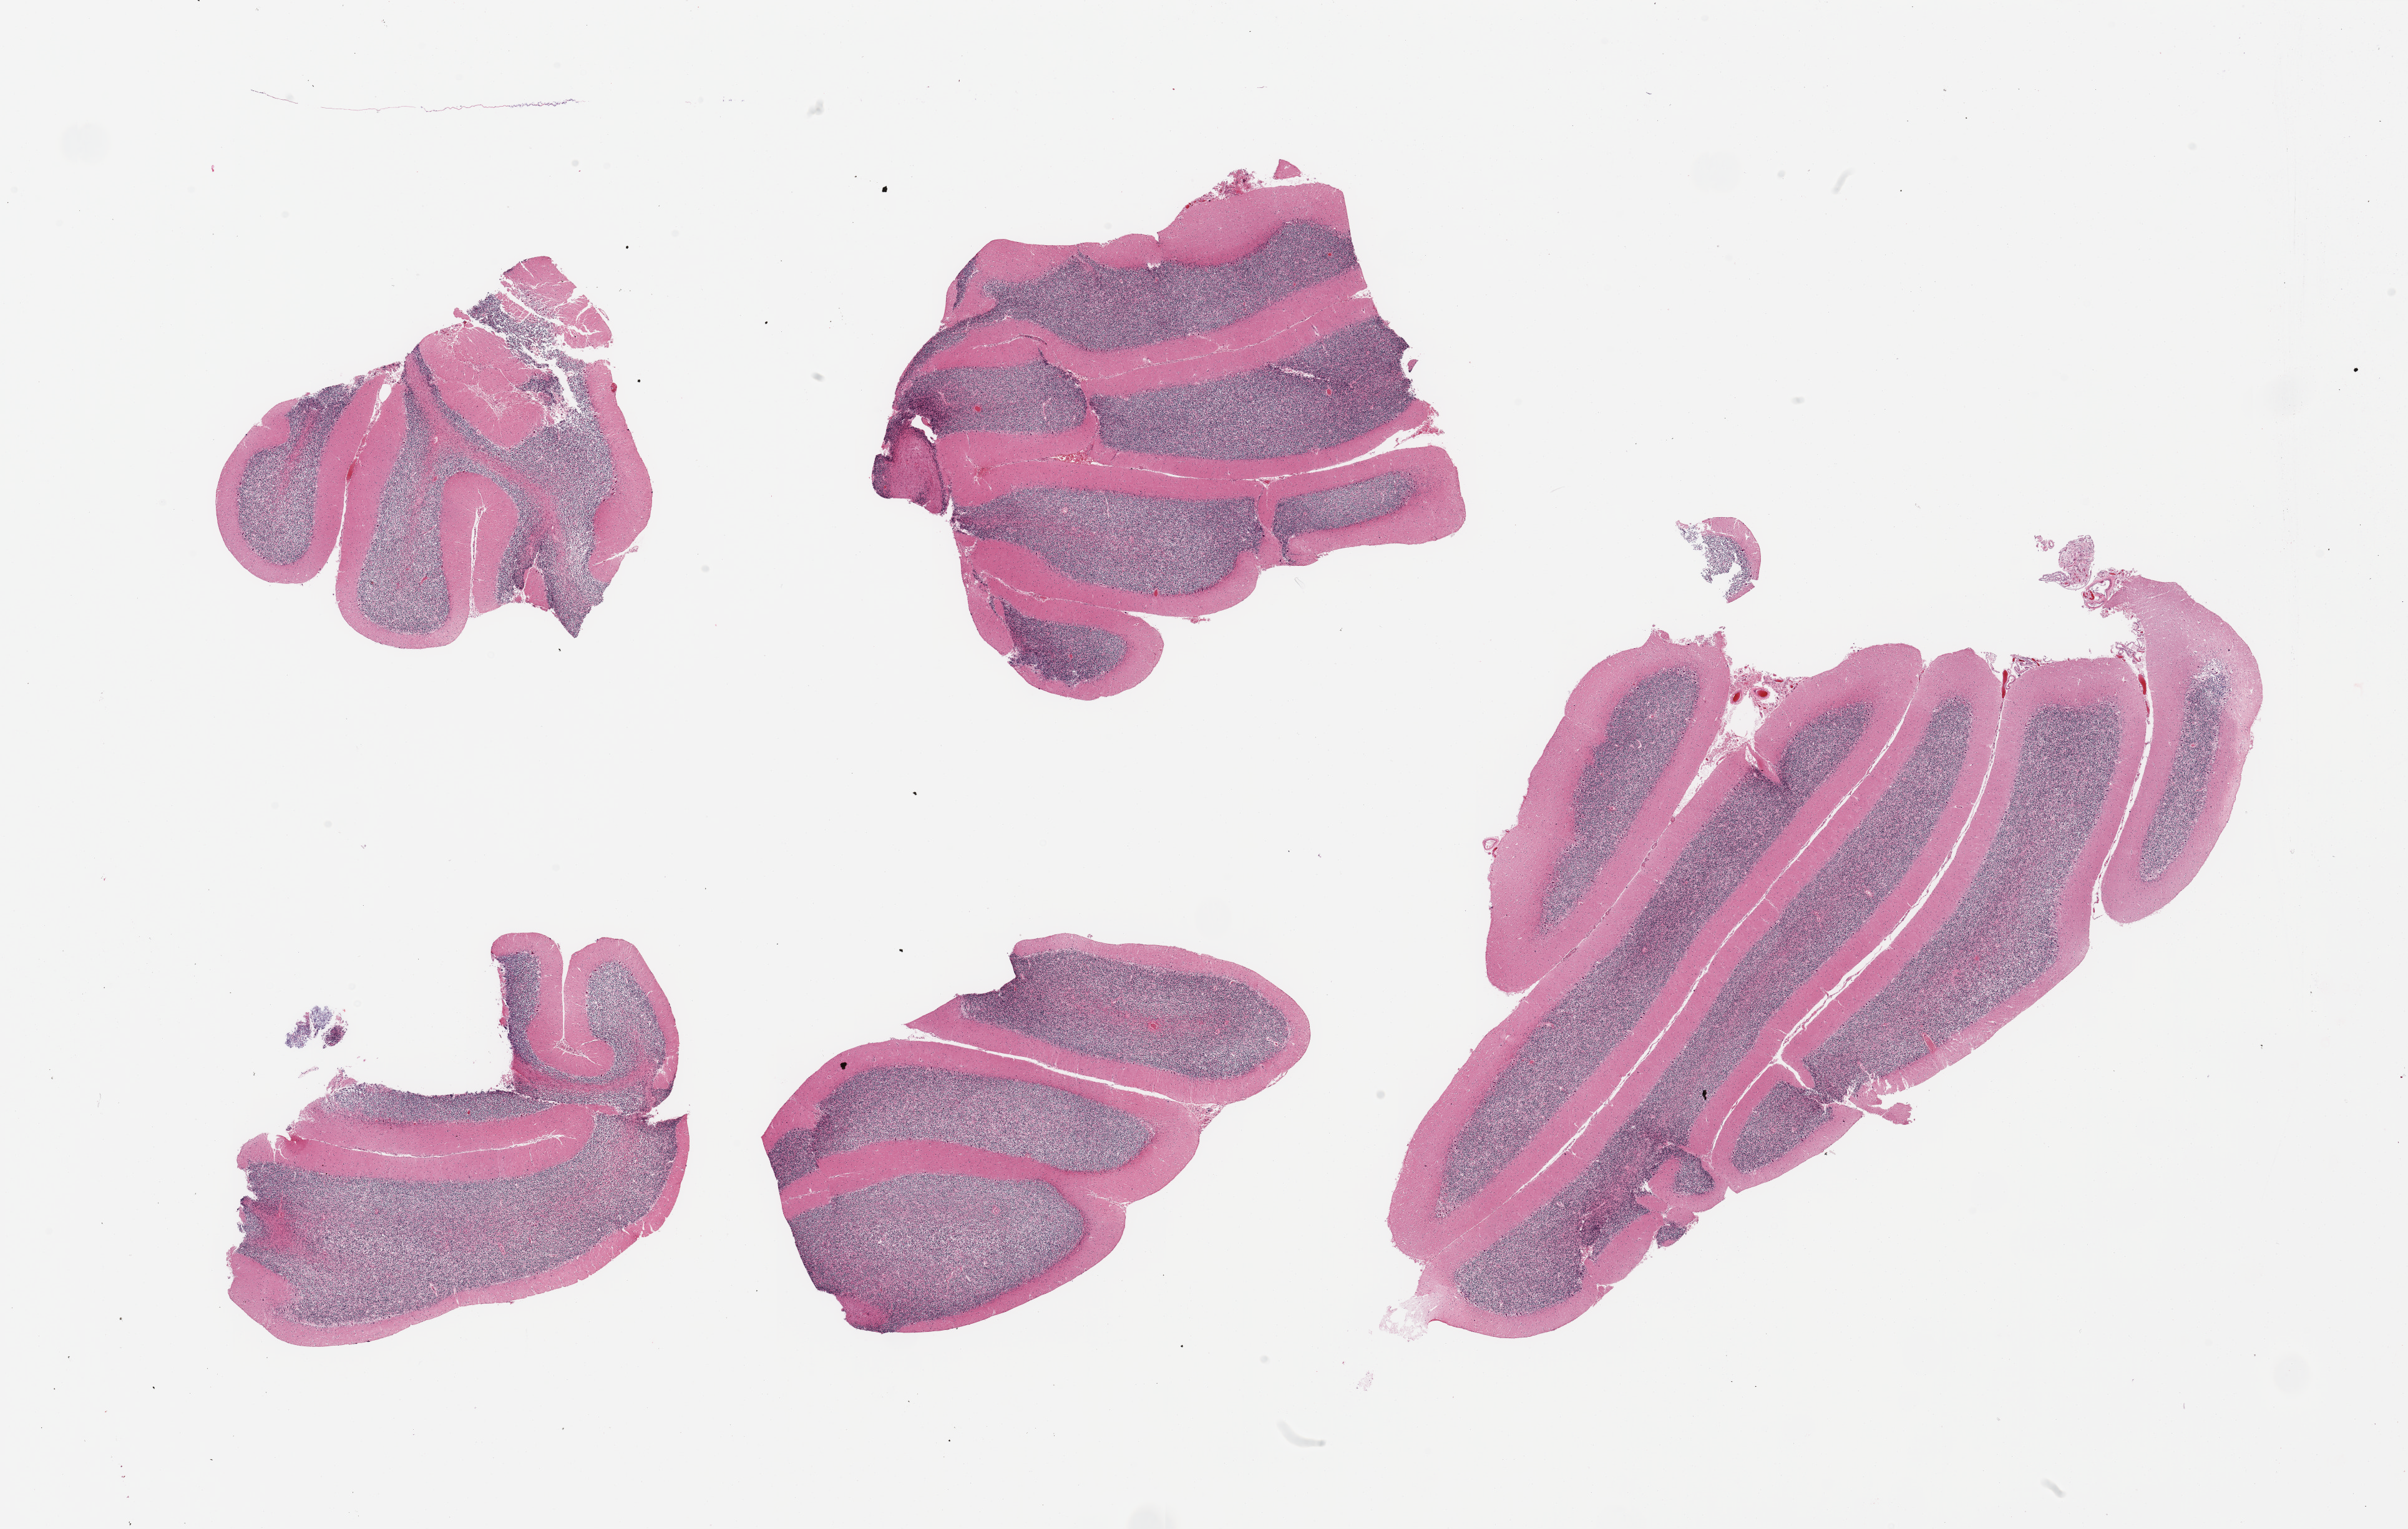
Digitized H&E-stained section — whole scanned area (about 30.5 x 19.4 mm, slide scanned at 20x) shown as a low-resolution overview, PAXgene-fixed paraffin-embedded (PFPE) section, section of cerebellum (target tissue), donor tissue sample. Donor sex: female.
Pathologist's review note for this sample: 5 pieces, no abnormalities.